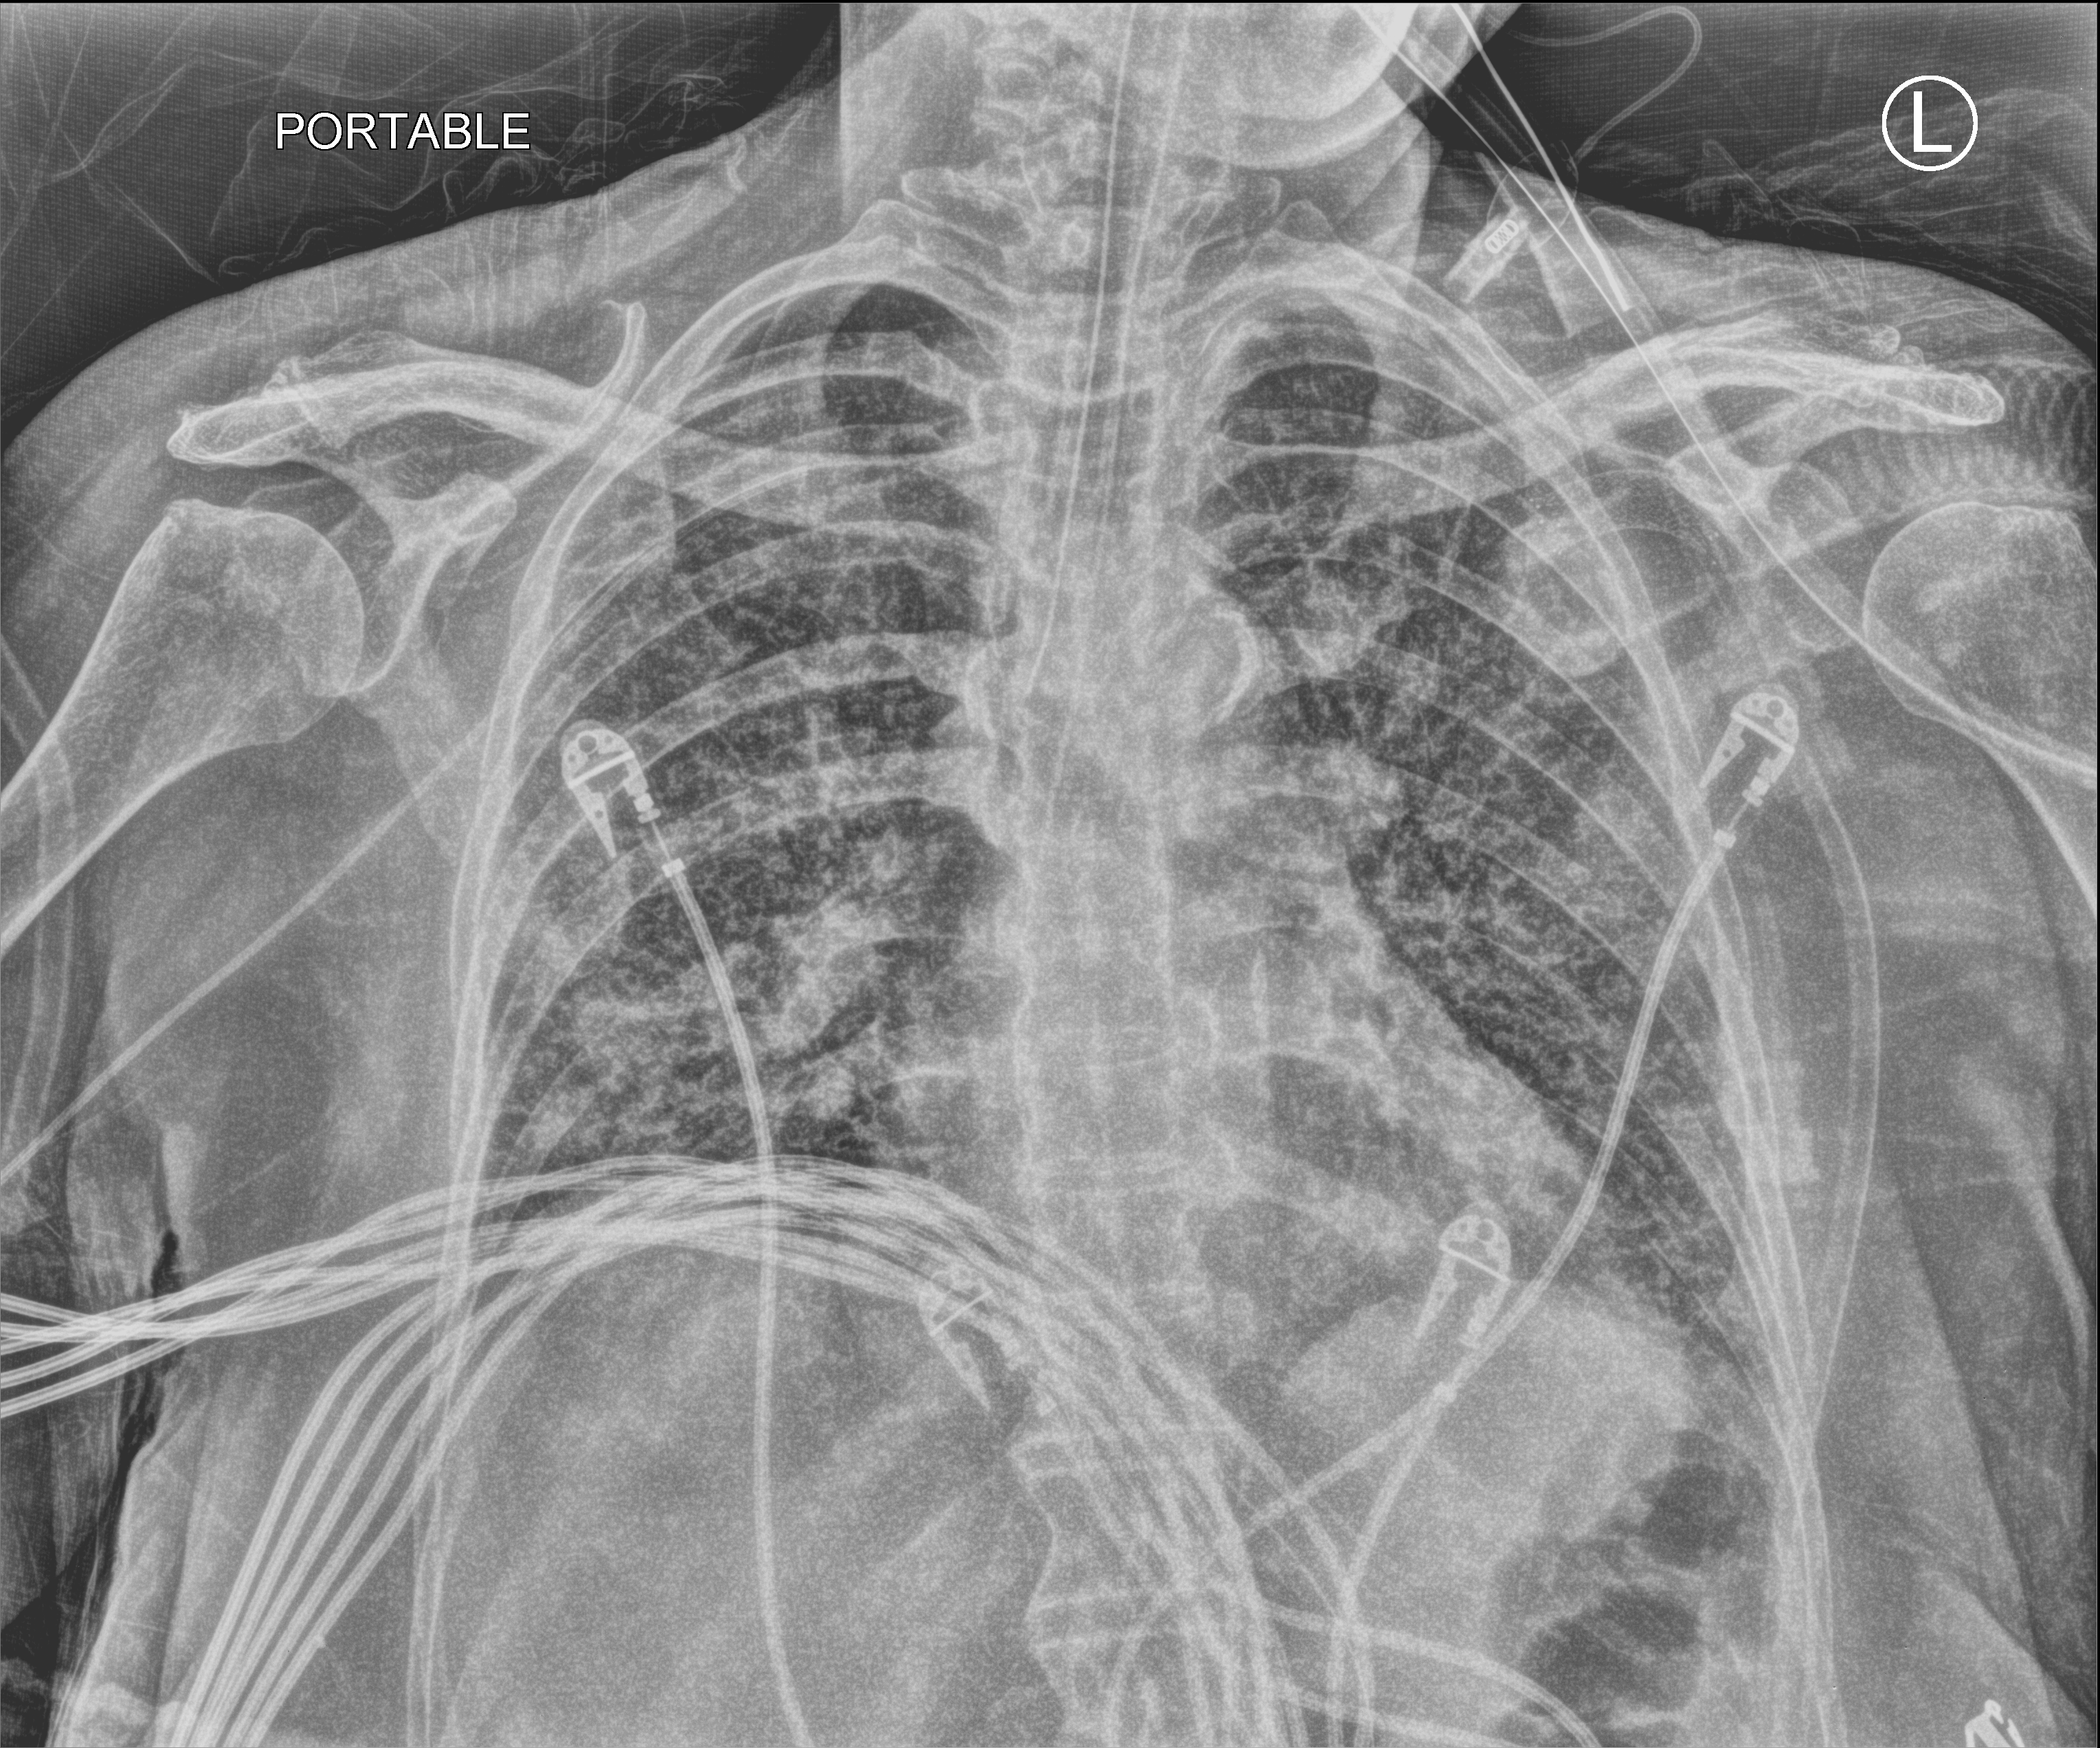
Bedside chest radiograph (computed radiography), anteroposterior (AP) projection. Female patient hospitalised with COVID-19, age 60–74 years.
From the hospital-stay record, not from the radiograph (when in the stay this image was taken is not recorded): mechanically ventilated during this hospital stay: yes.